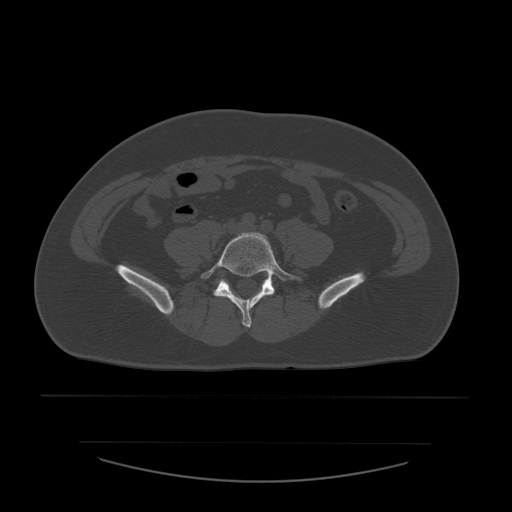
CT including the spine, one axial slice. Position 120 of 532 along the scan axis. Reconstruction kernel STANDARD. Bone window (W 1800 / L 400 HU). 1.25 mm slice thickness. 512 × 512 image matrix. Patient age 44 years. Case-level facts recorded for this patient, not image findings: primary cancer: soft tissue sarcoma.
Structures marked on this image (semi-automatically segmented with operator editing):
- L5 vertebra: bounding box [x1, y1, x2, y2] px = [201, 233, 301, 328]